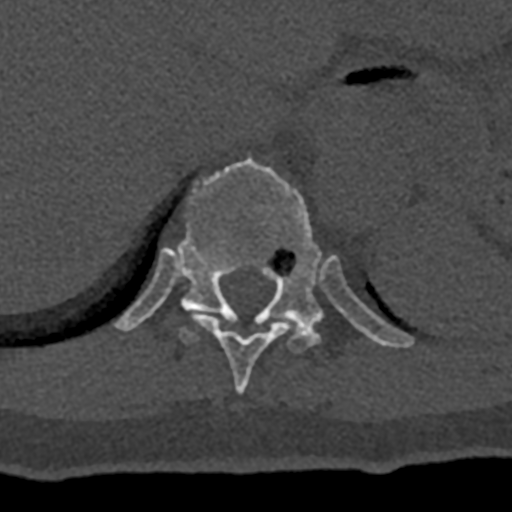
CT including the spine, one axial slice. Reconstruction kernel Br40s/3. 120 kVp. Bone window (W 1800 / L 400 HU). 512 × 512 image matrix, field of view 160 × 160 mm. Patient: male, 74 years. Case-level facts recorded for this patient, not image findings: primary cancer: renal.
Structures marked on this image (semi-automatically segmented with operator editing):
- T10 vertebra: bounding box (x1, y1, x2, y2) in pixels: (192, 314, 290, 394)
- T11 vertebra: (115, 158, 414, 353)